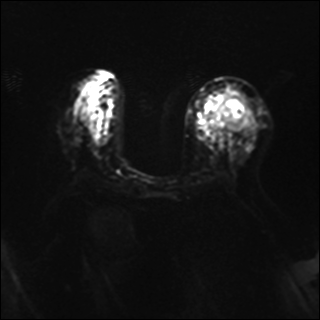
Breast MRI, one axial slice. Diffusion-weighted series; image 2 of 4 stored at this slice position (different b-values; order by instance number). 1.5 T. 4 mm slice thickness. 320 × 320 image matrix. Female patient.
Structures marked on this image (manually delineated by an expert):
- tumour on diffusion-weighted imaging: bounding box (x1, y1, x2, y2) in pixels: (223, 98, 242, 124)